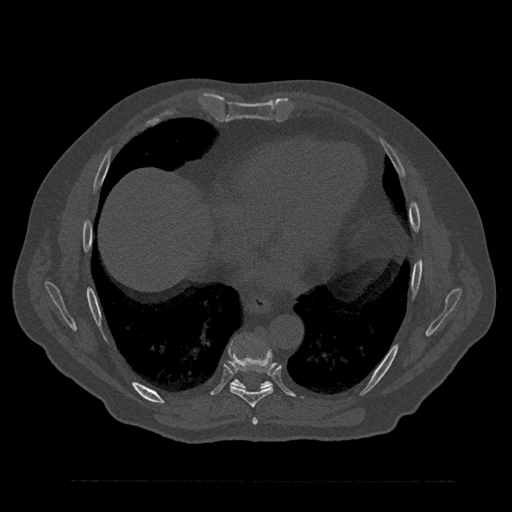
CT including the spine, one axial slice; slice 441 of 797 in the series (ordered by position); 120 kVp; bone window (W 1800 / L 400 HU); 512 × 512 image matrix. Male patient, age 61 years. Case-level facts recorded for this patient, not image findings: primary cancer: prostate.
Annotated regions visible in this slice (semi-automatic segmentation, software-assisted and operator-edited):
- T7 vertebra: bounding box [x1, y1, x2, y2] px = [252, 418, 258, 425]
- T8 vertebra: [229, 349, 276, 408]
- T9 vertebra: [231, 379, 272, 389]